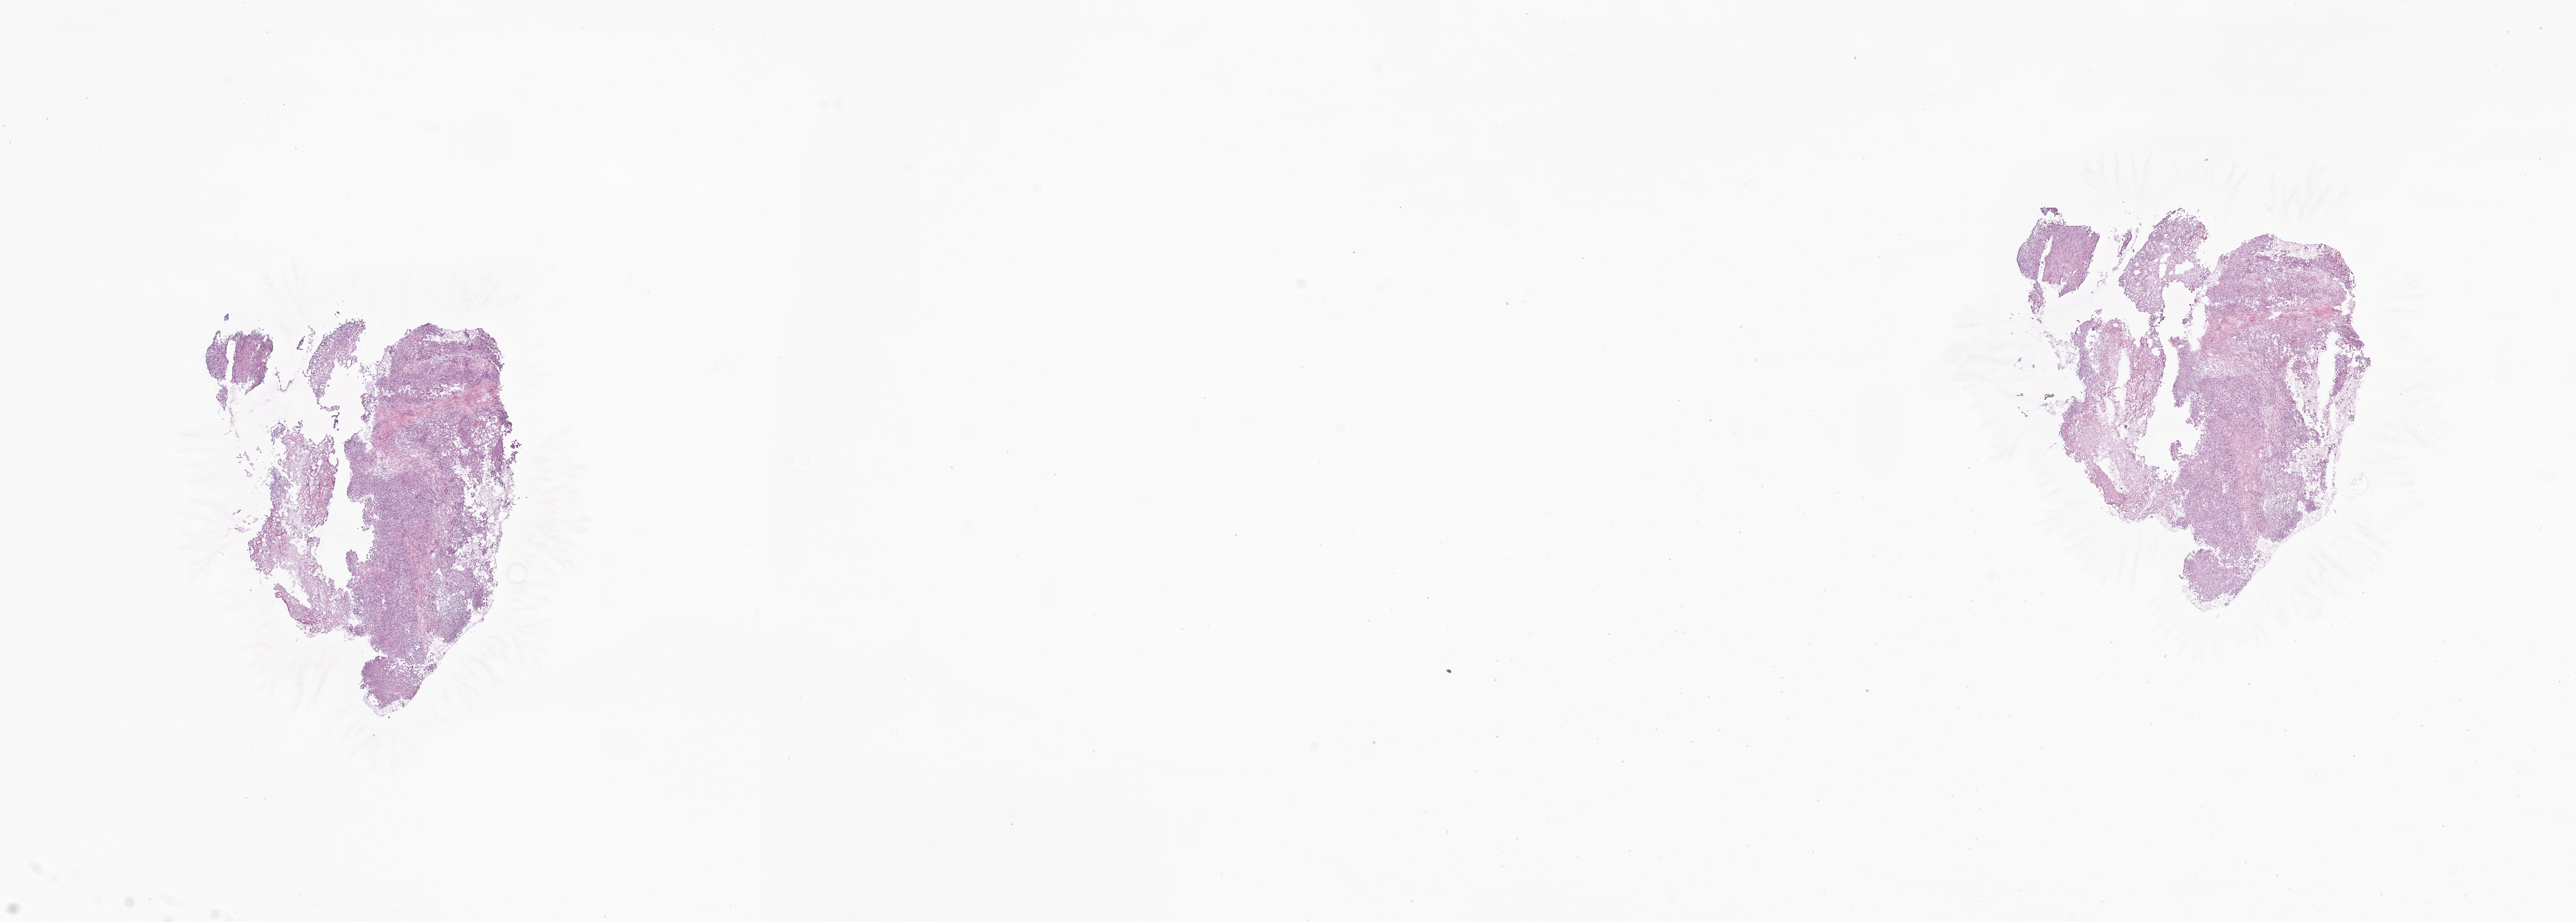
Whole-slide image, haematoxylin and eosin stain of tumor tissue from the soft tissue of lower extremity, a low-resolution overview of the entire scanned area, about 24.3 x 8.7 mm, frozen section. Patient: female, age 237 months.
Tissue or organ of origin (case record): connective, subcutaneous and other soft tissues of lower limb and hip. Diagnosis (ICD-O-3 morphology term): Epithelioid sarcoma, NOS.